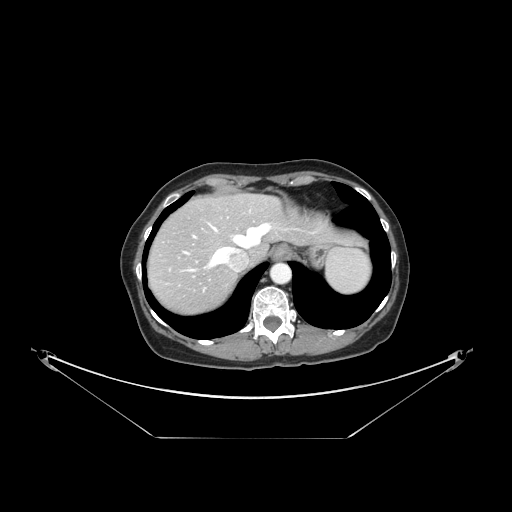
Contrast-enhanced abdominal CT, one axial slice. 120 kVp. Intravenous contrast given. Soft-tissue window (W 400 / L 40 HU). 2.5 mm slice thickness. 512 × 512 image matrix, field of view 500 × 500 mm. Female patient, age 73 years. From the clinical record (not read from this slice): diagnosis: colorectal cancer liver metastases, imaged before liver resection.
Outlined on this slice (expert manual segmentation):
- hepatic veins: box from (x=187, y=223) to (x=298, y=267) px
- liver: (x=149, y=196)–(x=331, y=313)
- planned liver remnant (the part of the liver to remain after resection): (x=176, y=196)–(x=332, y=260)